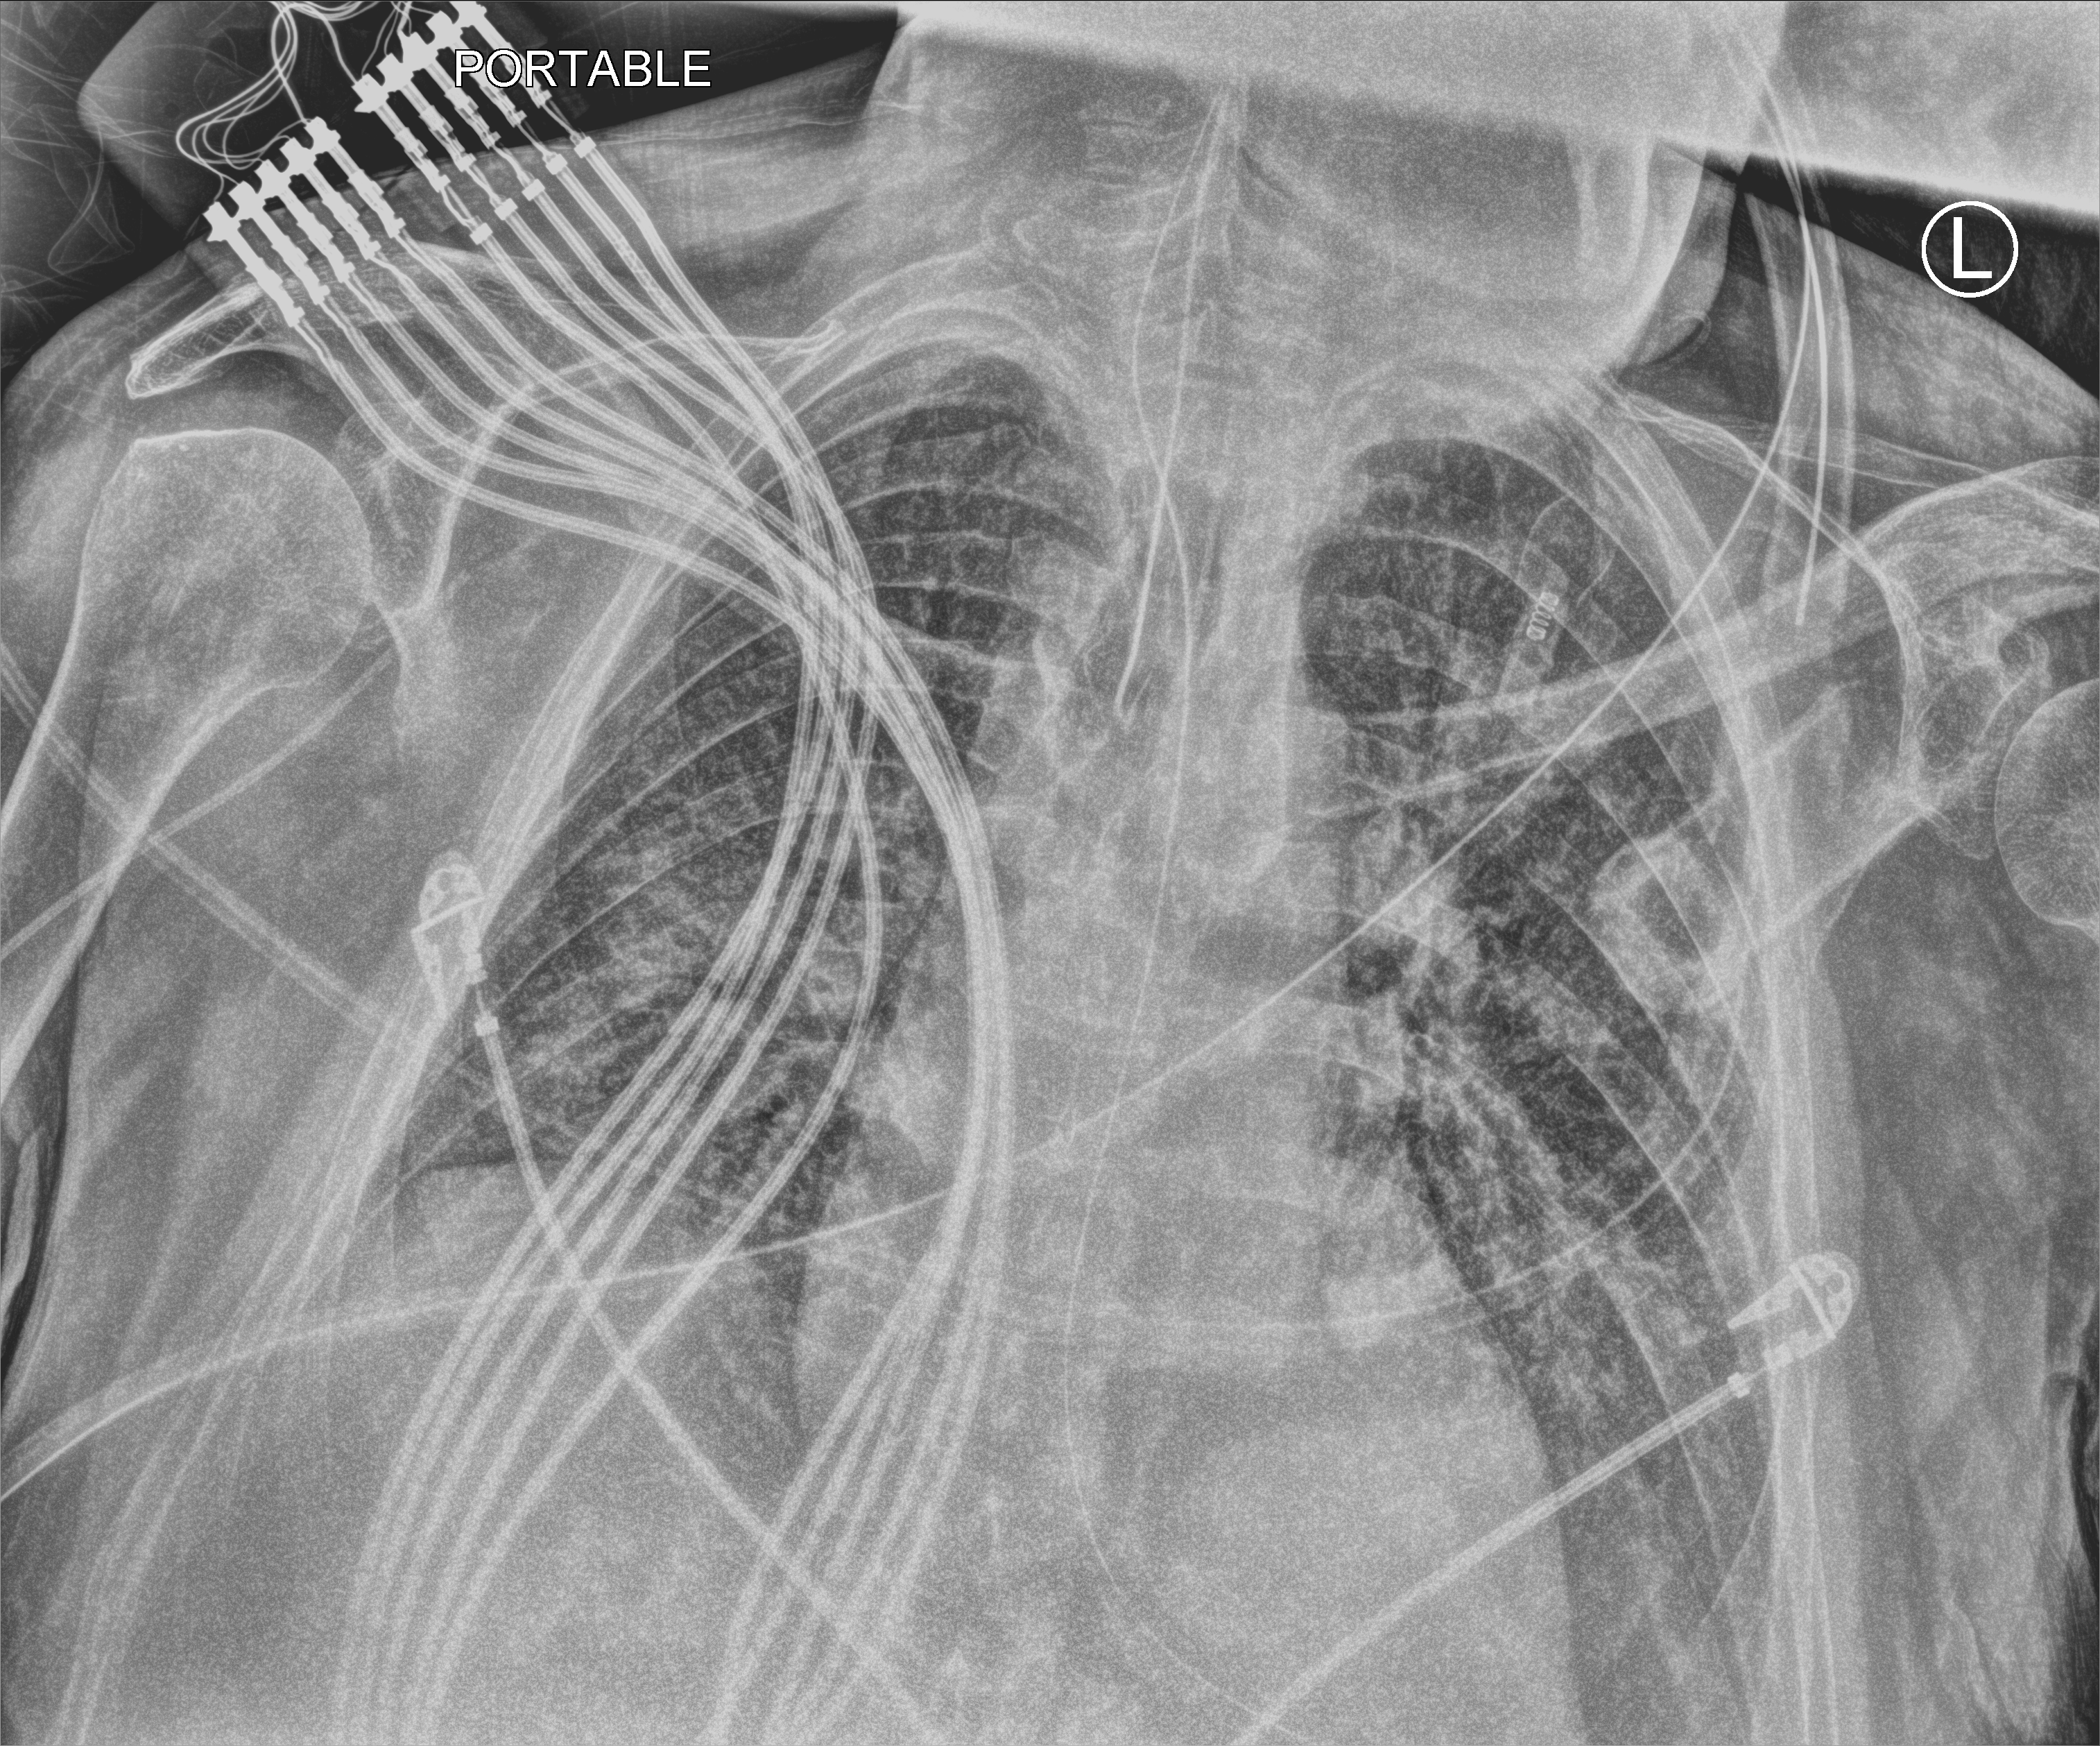
Bedside chest radiograph (computed radiography), anteroposterior (AP) projection. Patient hospitalised with COVID-19; male, aged 60–74 years.
From the hospital-stay record, not from the radiograph (when in the stay this image was taken is not recorded):
- mechanically ventilated during this hospital stay: yes
- admitted to intensive care during this hospital stay: yes